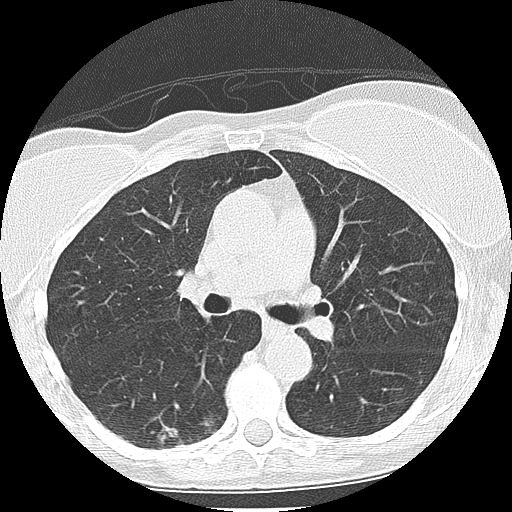
Low-dose screening chest CT, one axial slice. Position 127 of 225 along the scan axis. 120 kVp. Lung window (W 1500 / L -600 HU). 2.5 mm slice thickness. 512 × 512 image matrix.
Outlined on this slice (manually delineated by an expert):
- lesion 1 (tumor, lower lobe of right lung): bounding box (x1, y1, x2, y2) in pixels: (159, 426, 184, 448)